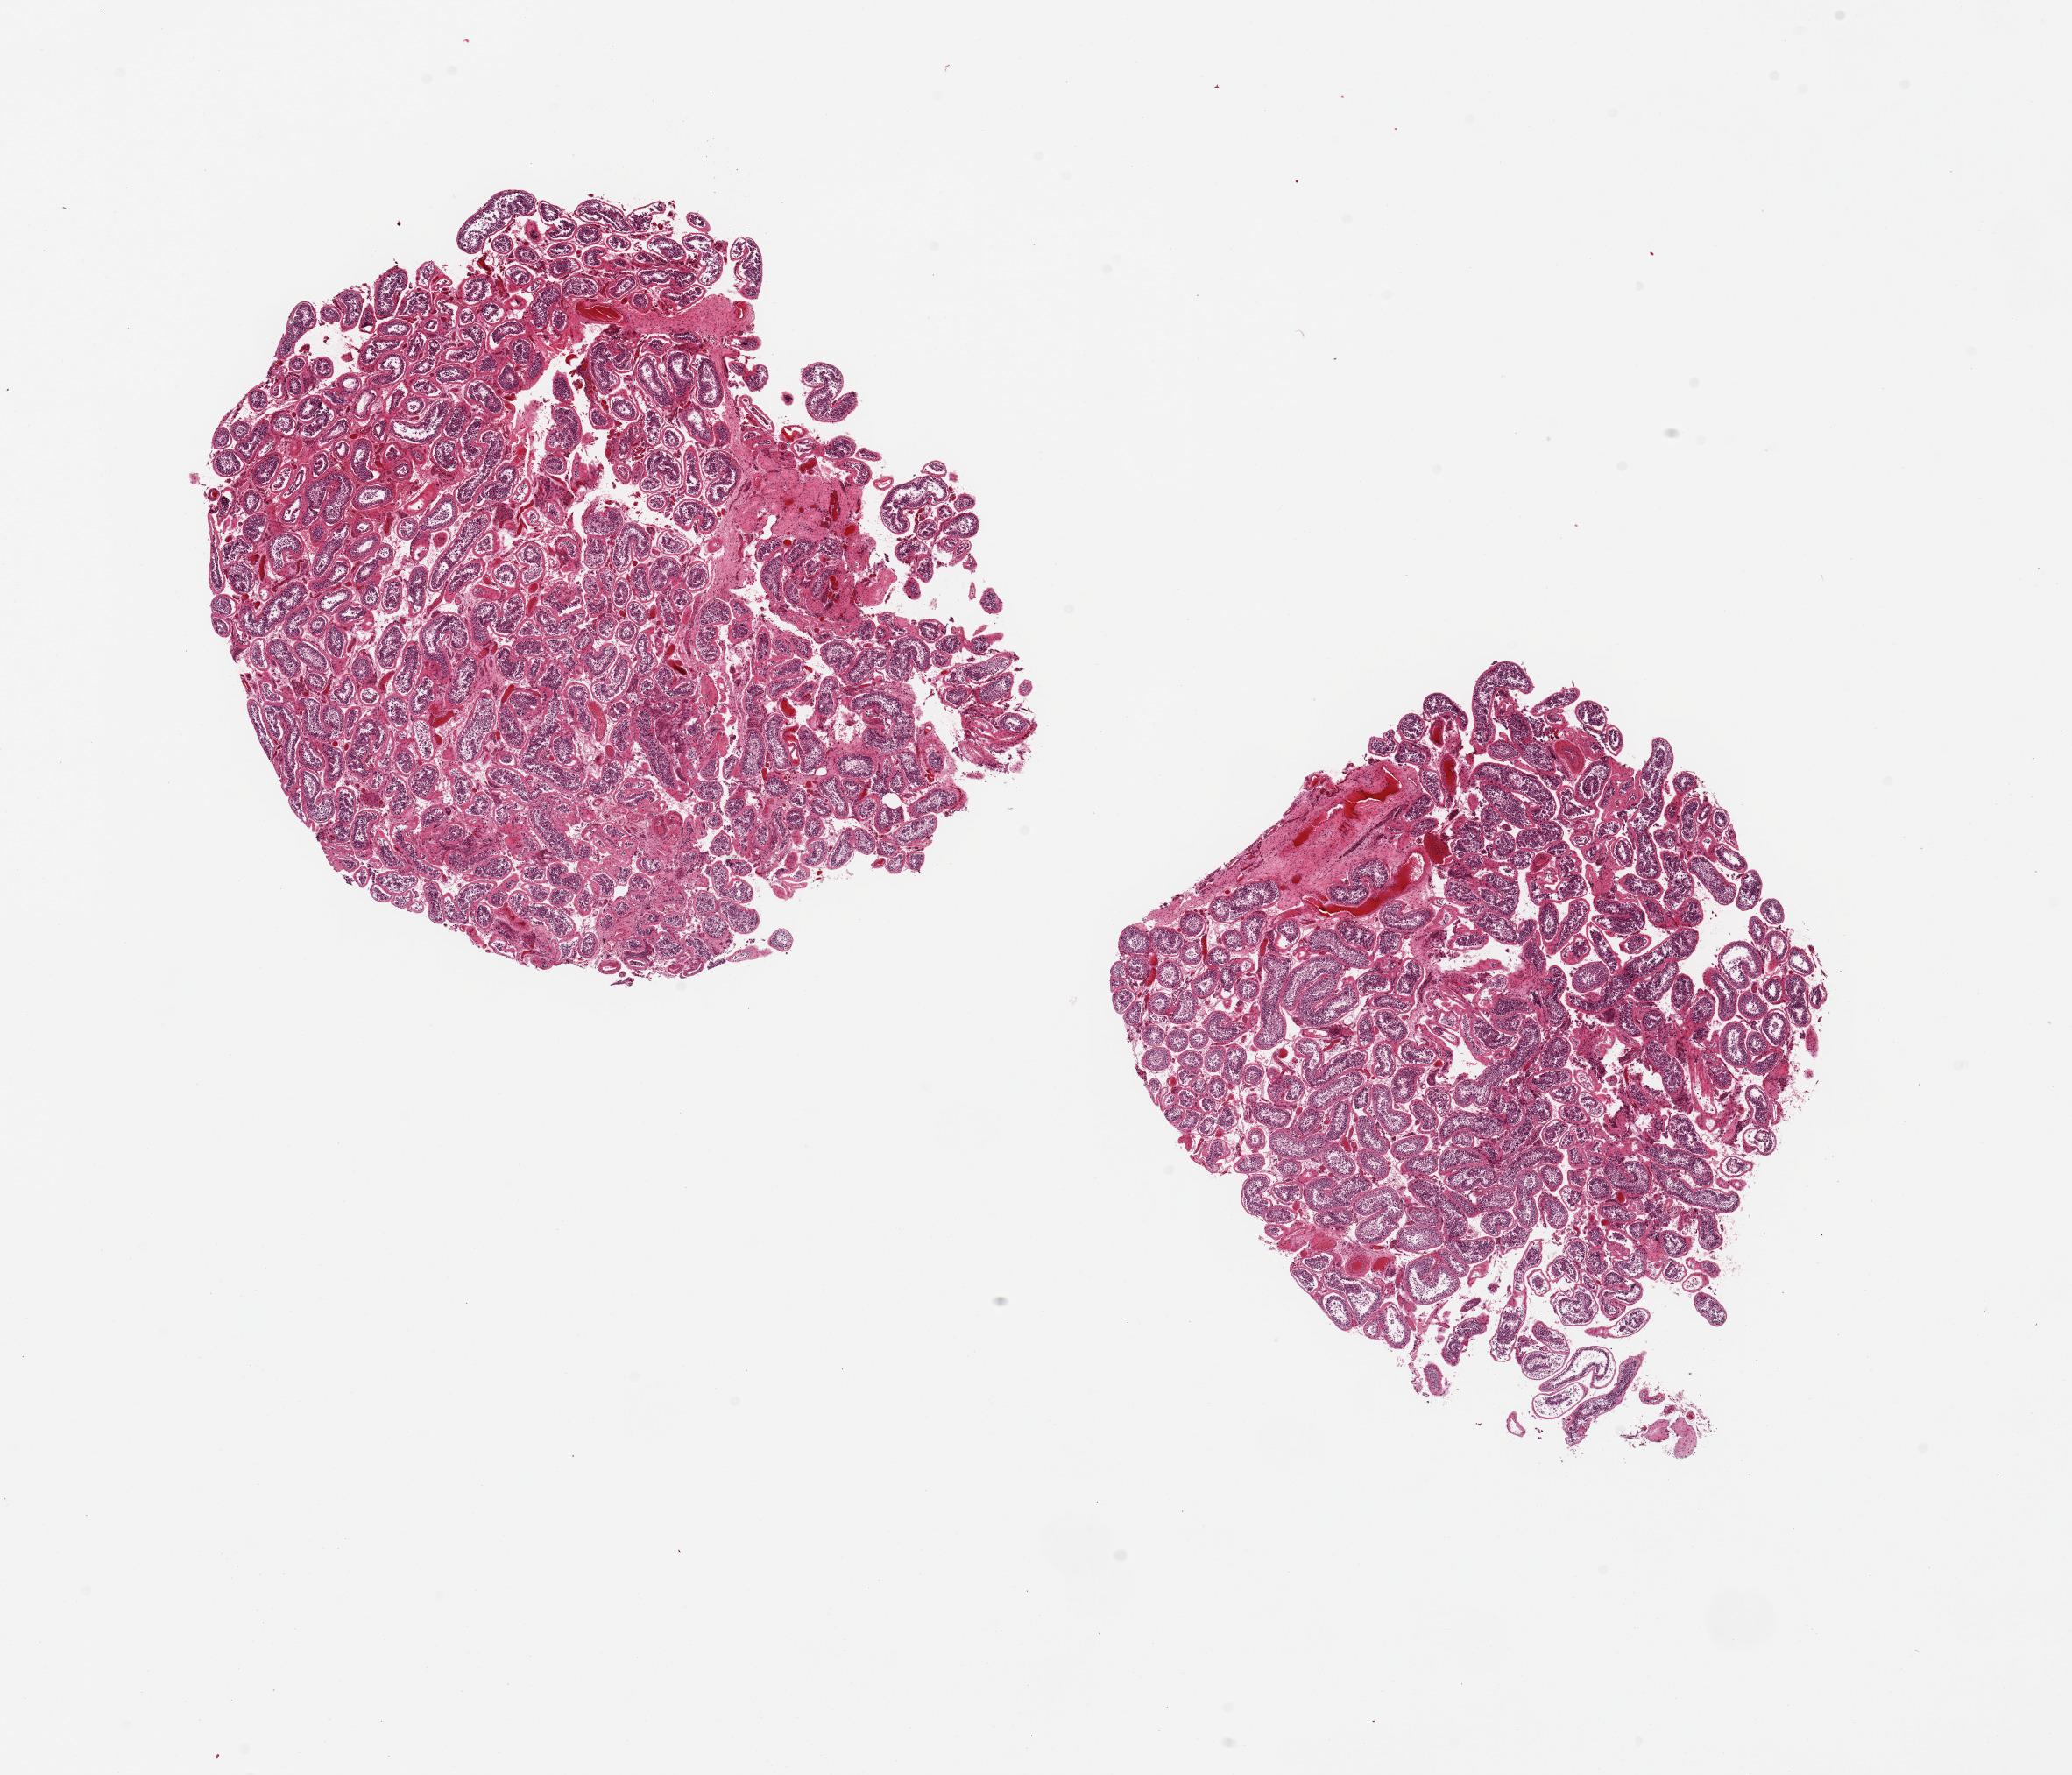
Whole-slide image, haematoxylin and eosin stain, shown as a low-resolution overview of the whole scanned area (about 18.7 x 16.0 mm, slide scanned at 20x), PAXgene-fixed, paraffin-embedded tissue, sampled site (target tissue): testis, donor tissue sample. Male donor.
Pathologist's review note for this sample: 2 pieces, reduced spermatogeneisis.